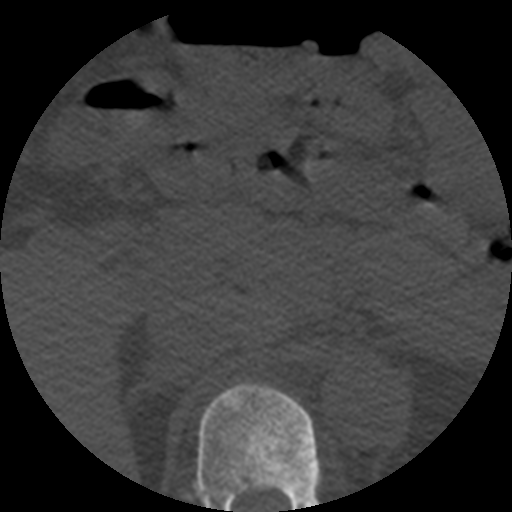
CT including the spine, one axial slice; slice 242 of 508 in the series (ordered by position); bone window (W 1800 / L 400 HU); 1.25 mm slice thickness; 512 × 512 image matrix, field of view 160 × 160 mm. Patient age 57 years. Case-level facts recorded for this patient, not image findings: primary cancer: prostate.
Annotated regions visible in this slice (semi-automatically segmented with operator editing):
- T11 vertebra: bounding box [x1, y1, x2, y2] px = [194, 383, 322, 512]